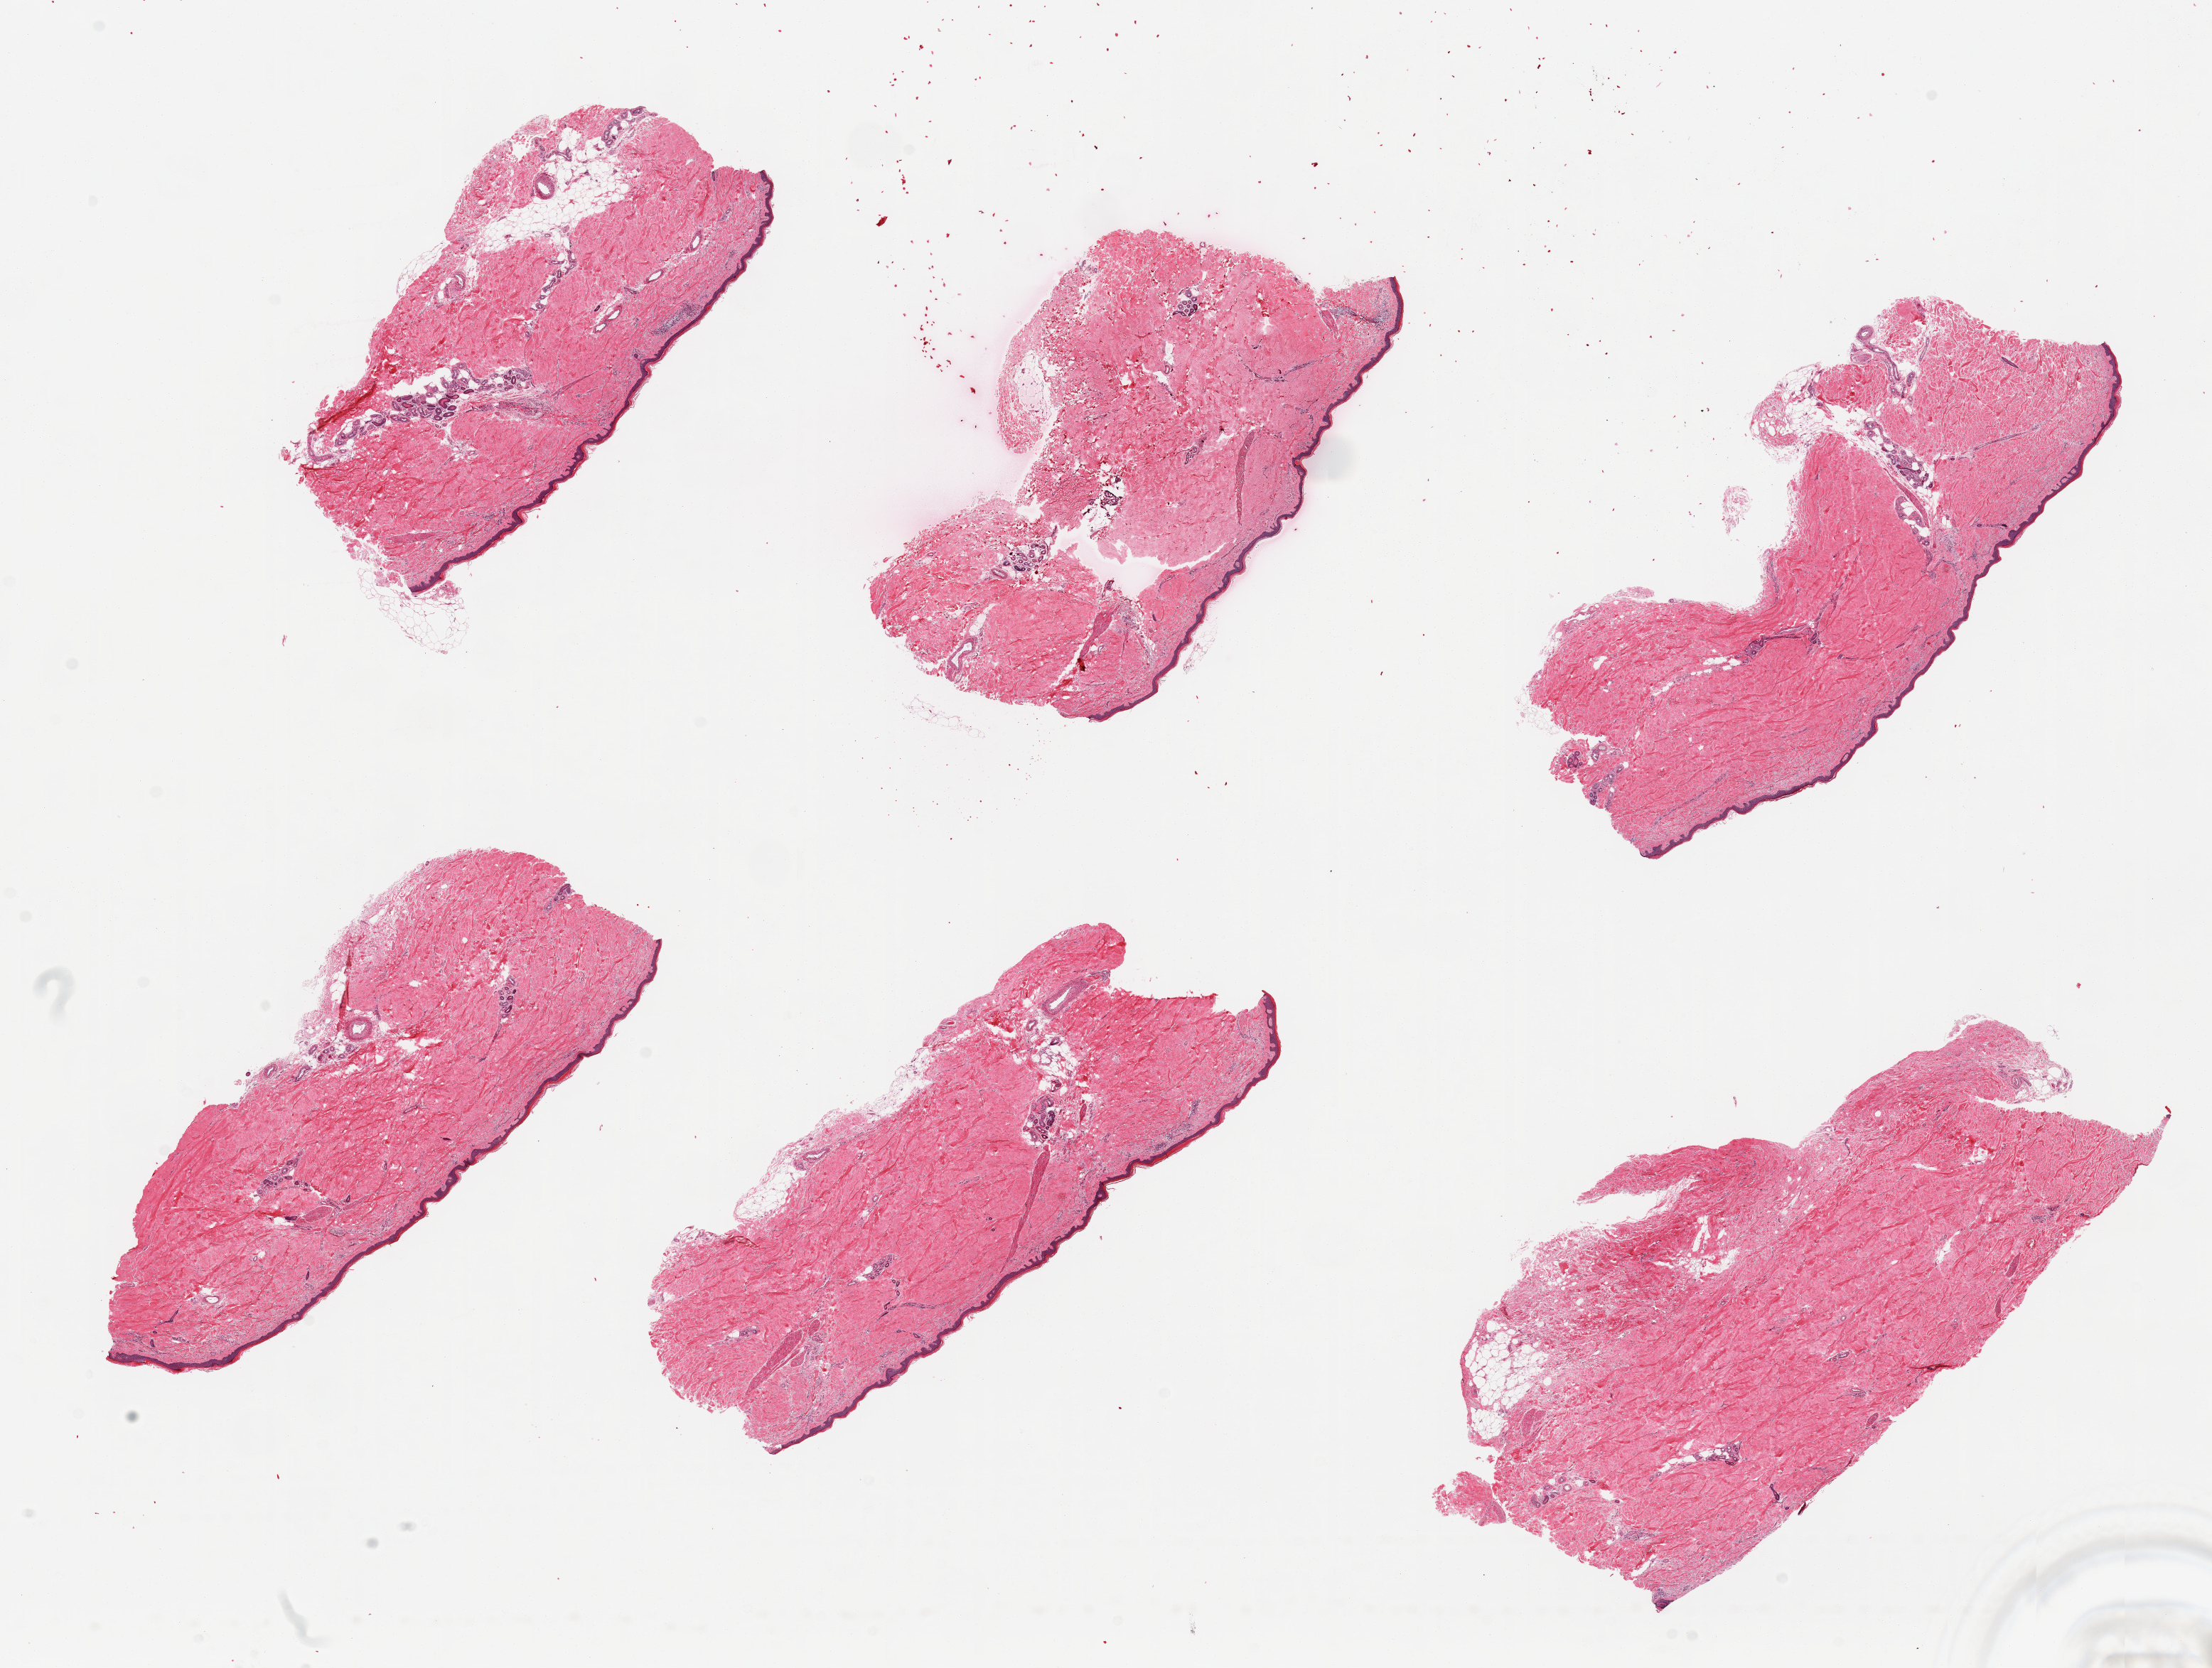
Haematoxylin and eosin whole-slide image, brightfield, shown as a low-resolution overview of the whole scanned area (about 24.6 x 18.6 mm). PAXgene-fixed, paraffin-embedded tissue. Sampled site (target tissue): skin of lower leg. Donor tissue sample. Male donor.
Review note (as recorded): 6 pieces; about 10% internal fat; one fragment devoid of epidermis; epidermis measures 53.1um thick.